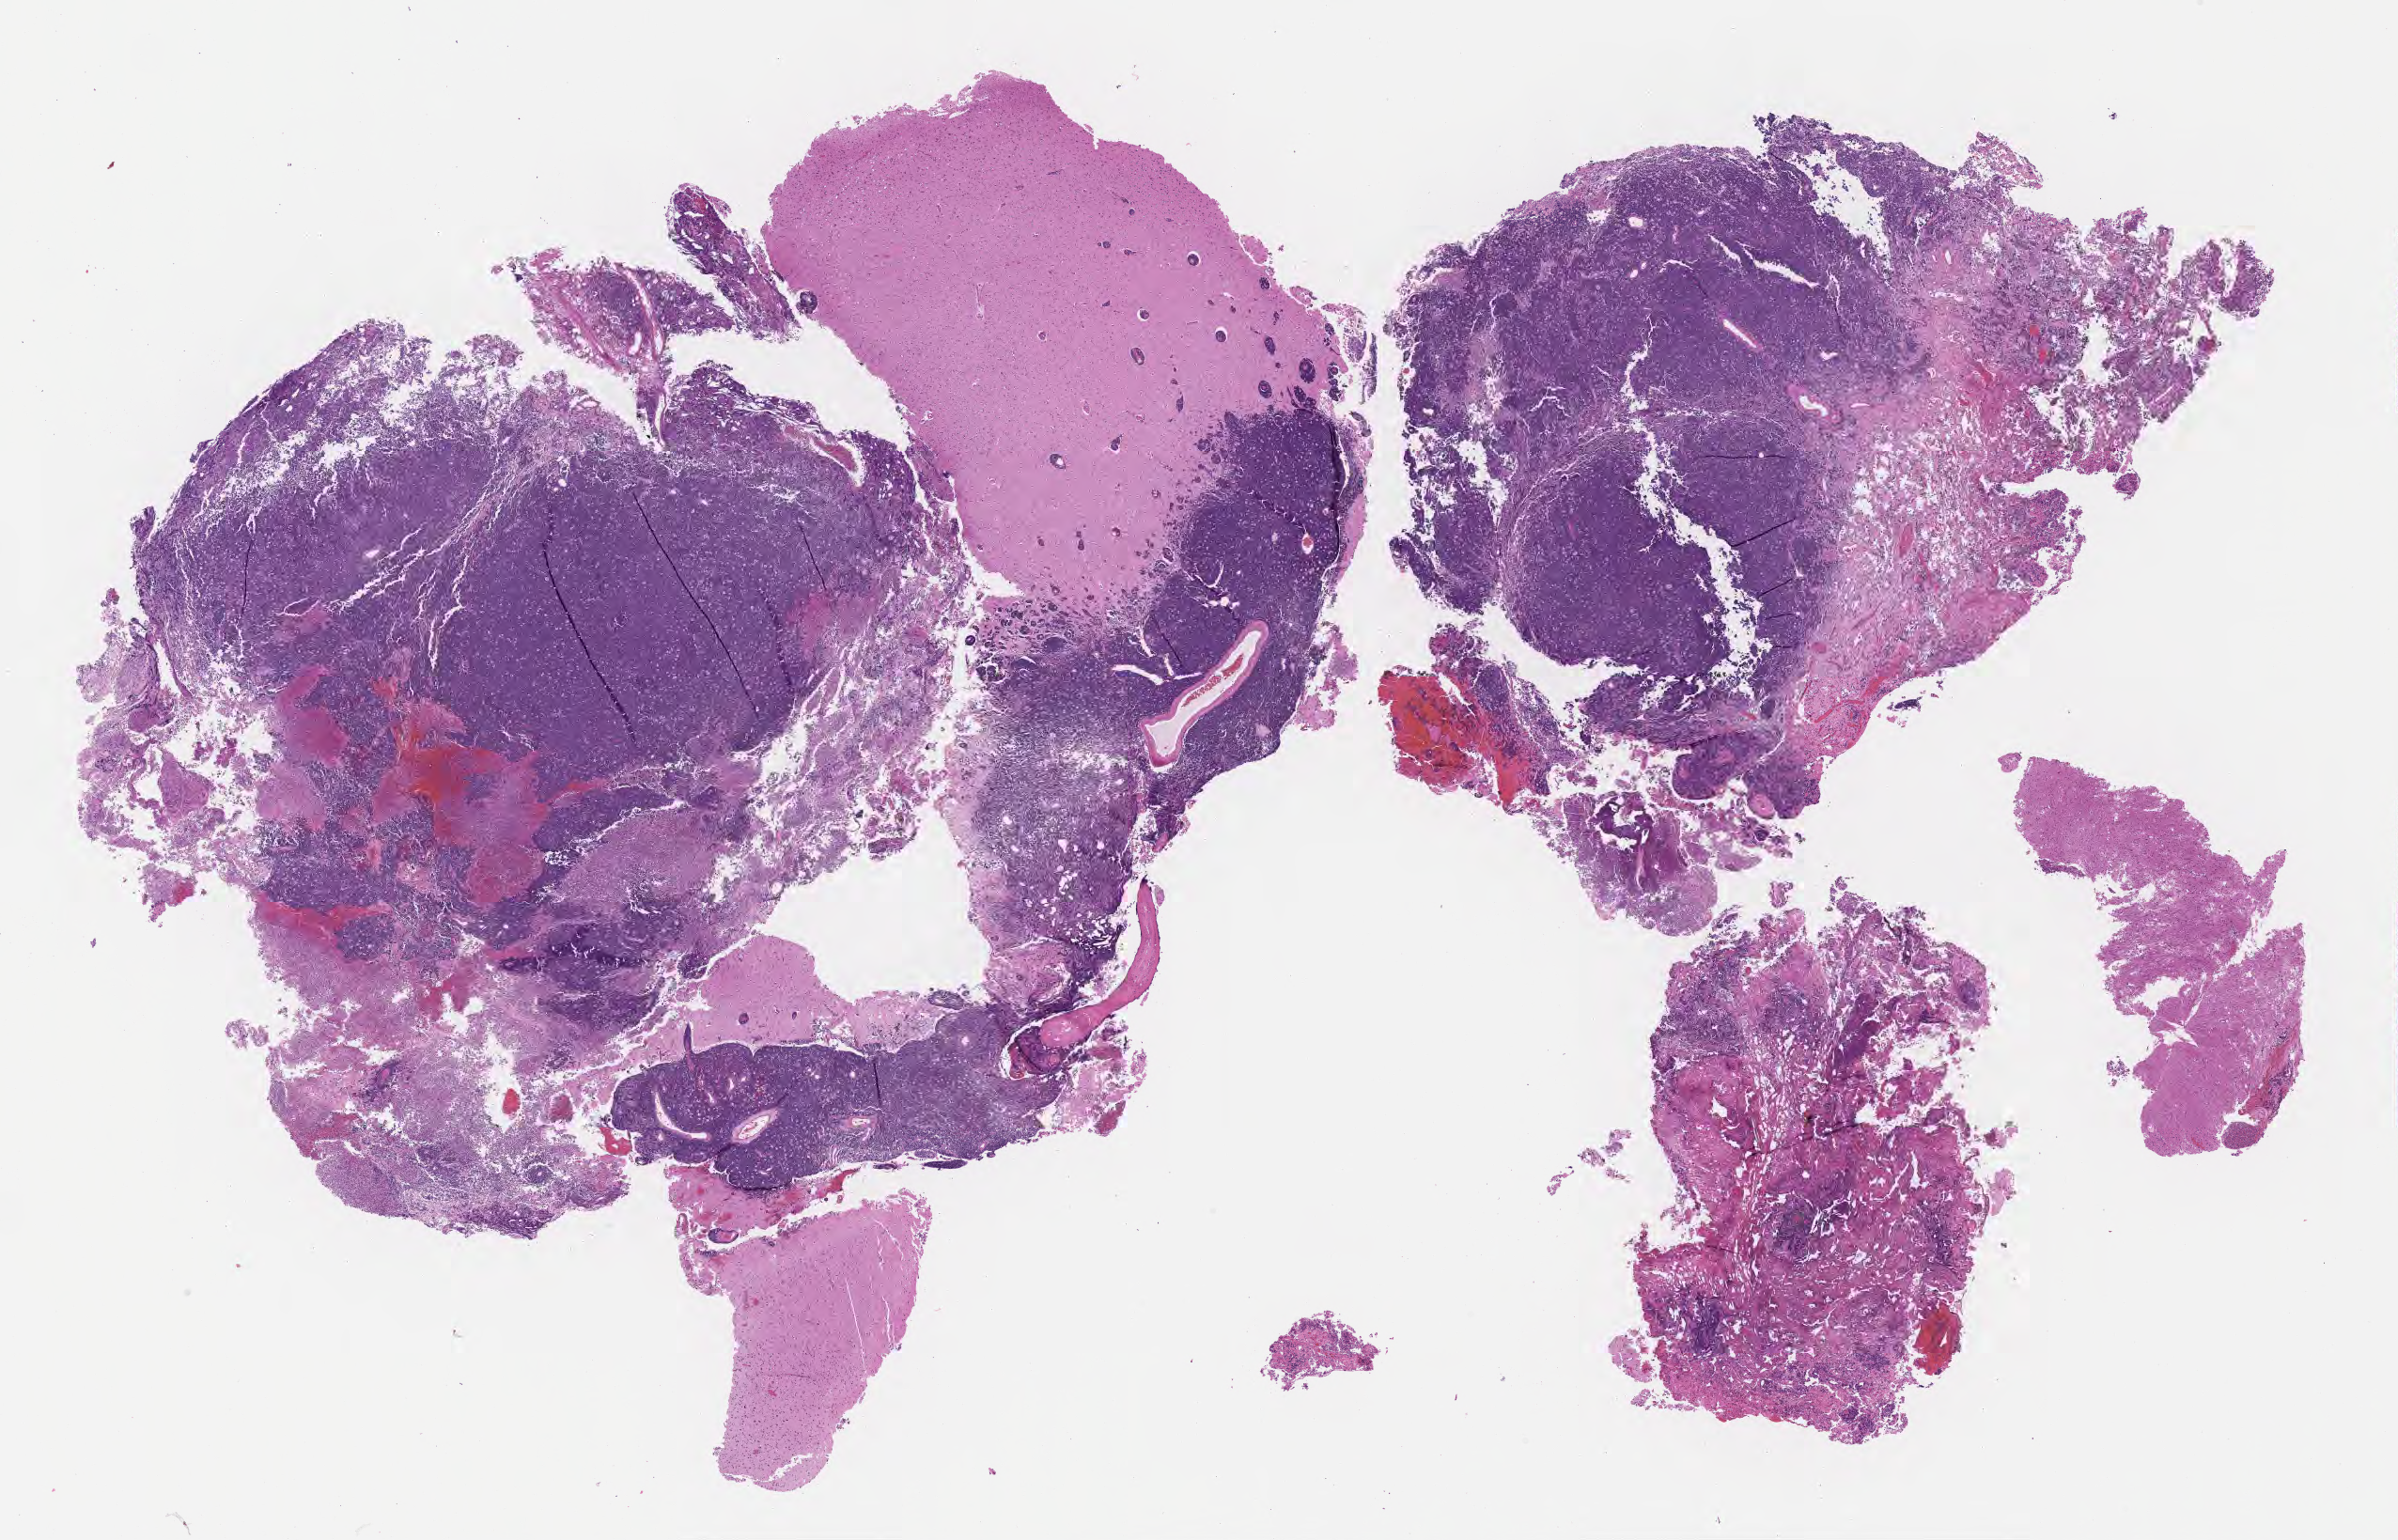
H&E whole-slide image, shown as a low-resolution overview of the whole scanned area (about 20.6 x 13.2 mm), specimen: tumor tissue. Female patient, 73 years old.
* diagnosis: Burkitt lymphoma, NOS